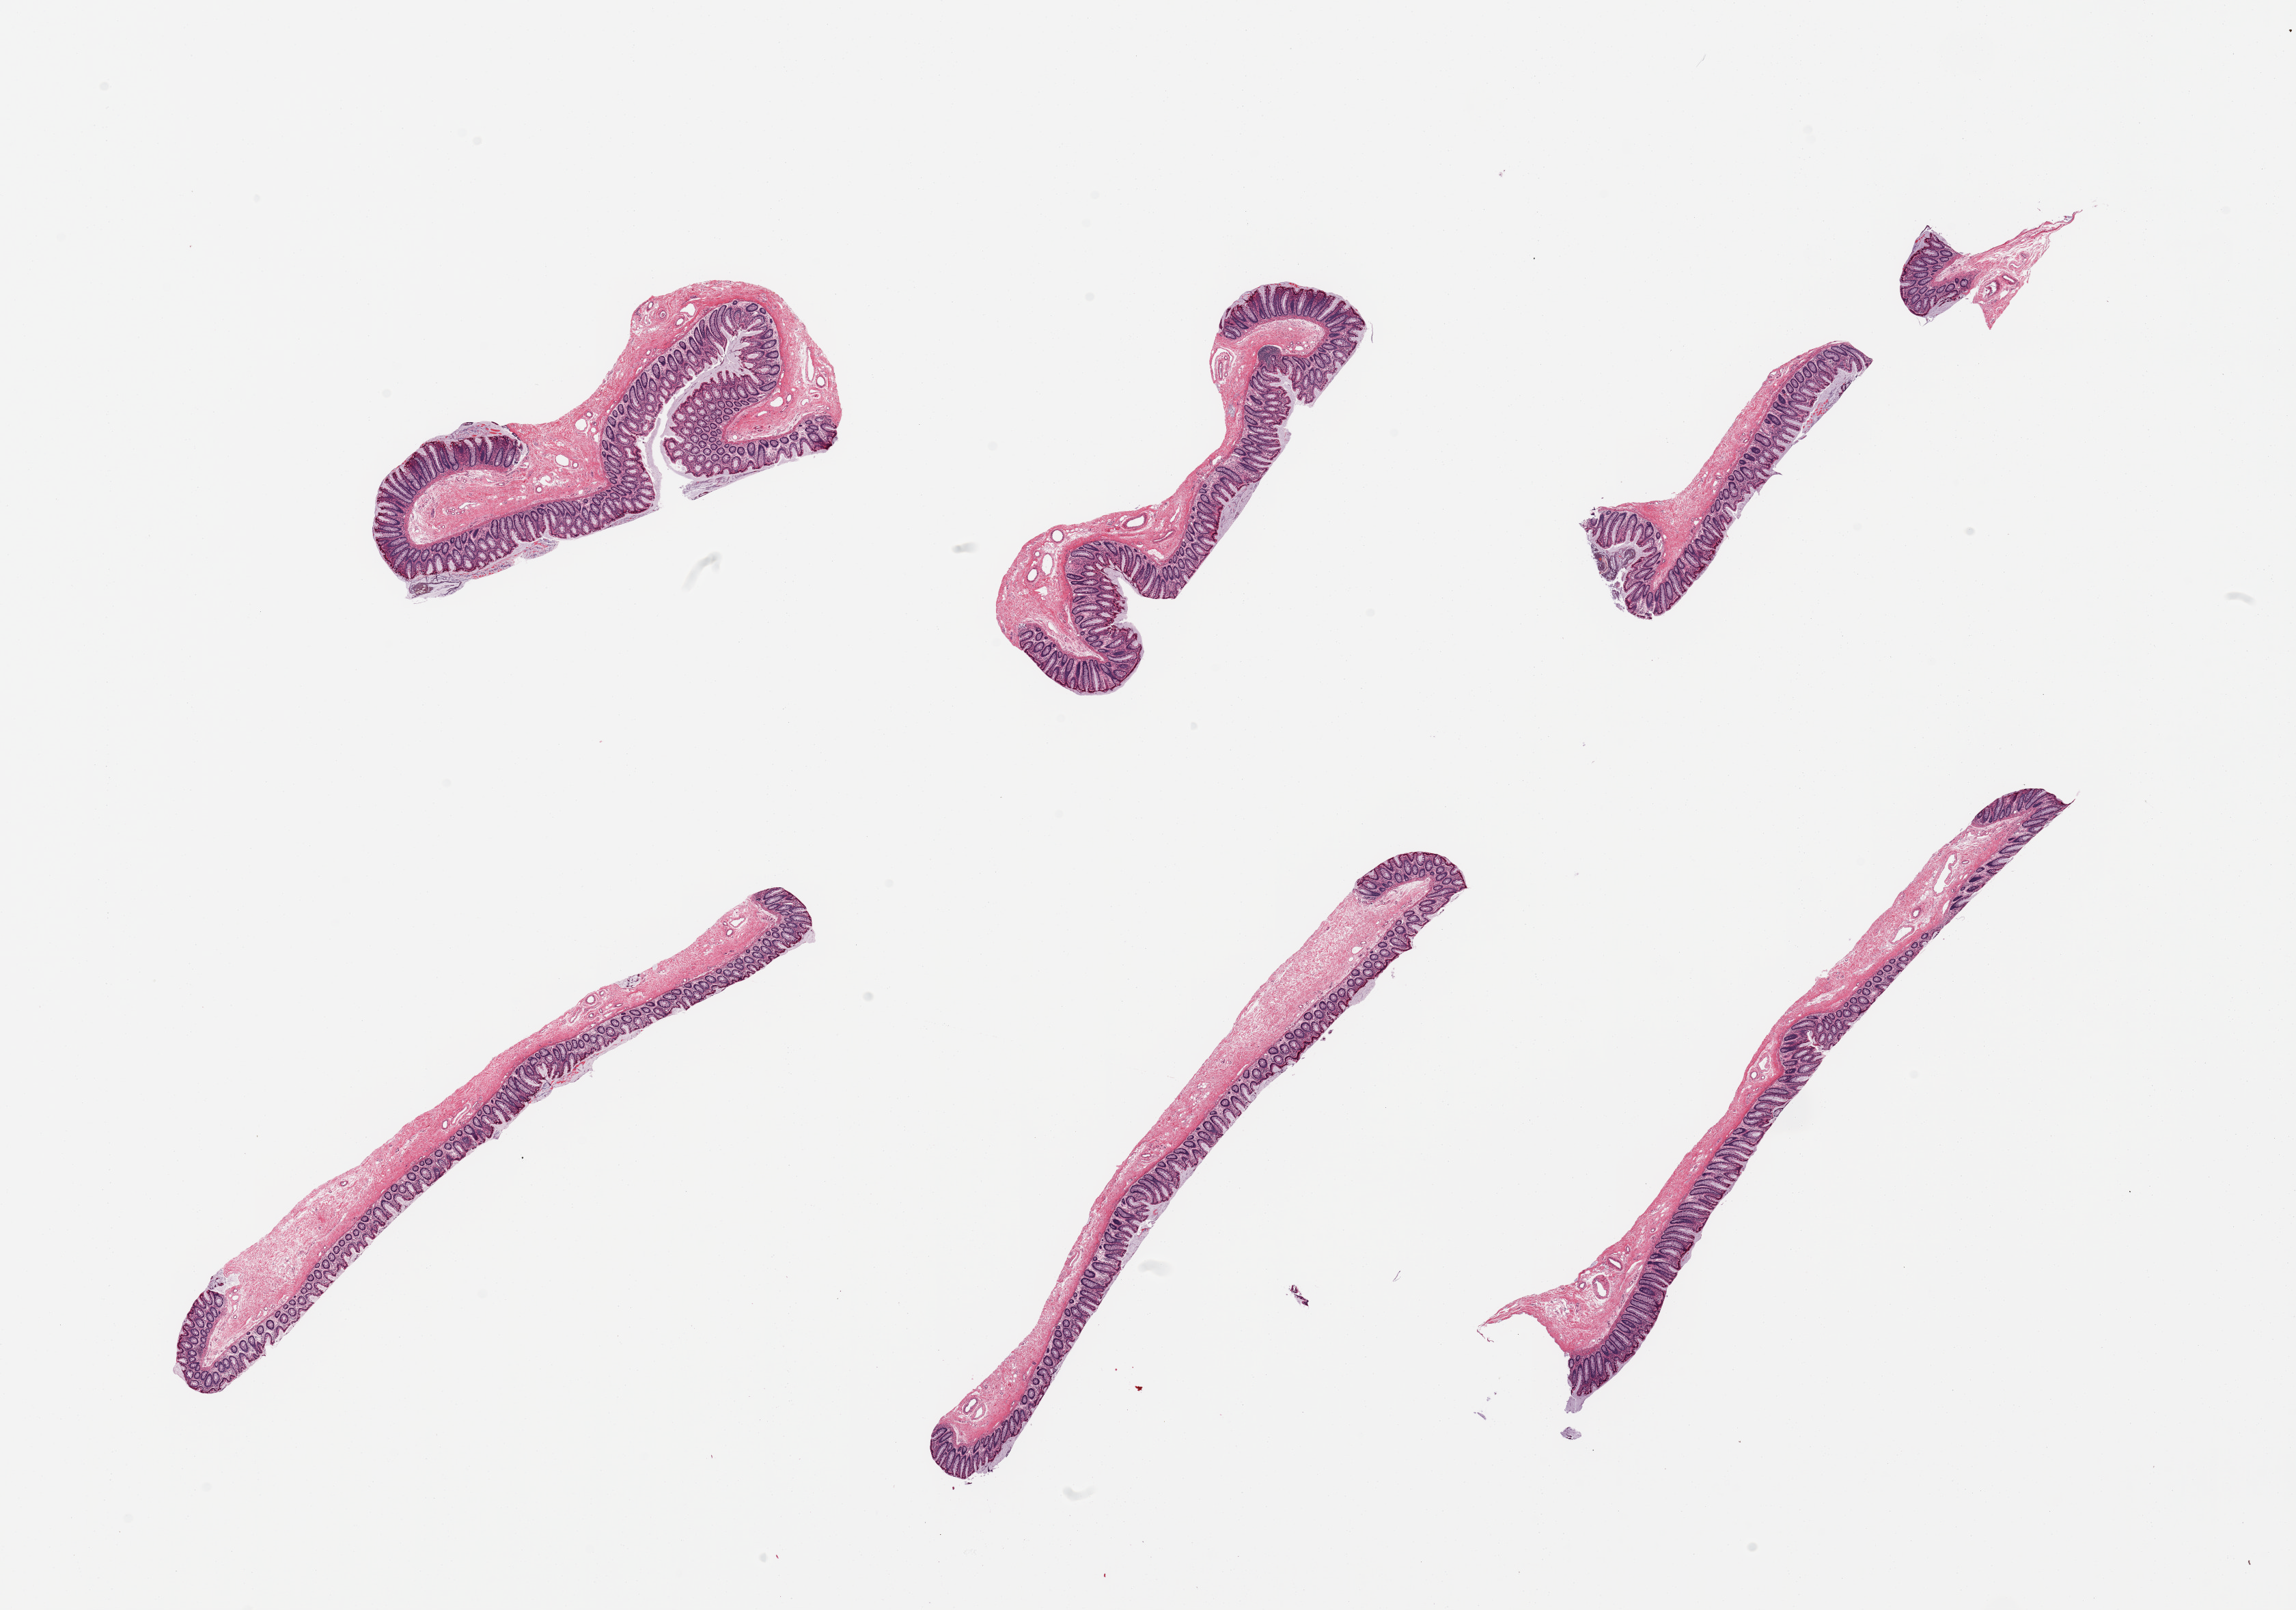
Haematoxylin and eosin whole-slide image — shown as a low-resolution overview of the whole scanned area (about 26.6 x 18.6 mm, slide scanned at 20x). PAXgene-fixed paraffin-embedded (PFPE) section. Sampled site (target tissue): transverse colon. Donor tissue sample. Donor: female.
Review note (as recorded): 6 pieces, mucosa fairly well preserved, ~0.3-0.4mm, up to ~40% thickness.